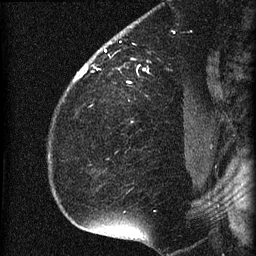
Breast MRI (dynamic contrast-enhanced), one sagittal slice; slice 48 of 60 in the series (ordered by position); dynamic contrast-enhanced series, image 2 of 4 at this slice position (ordered by acquisition); 1.5 T; TE 4.2 ms, TR 22.7 ms; 1.5 mm slice thickness; 256 × 256 image matrix, field of view 180 × 180 mm. Female patient, age 35 years. From the clinical record (not read from this slice): setting: breast cancer imaged before/during neoadjuvant chemotherapy; receptor status: HR-positive, HER2-negative.
Annotated regions visible in this slice (semi-automatic segmentation, software-assisted and operator-edited):
- analysis volume of interest (the breast-tissue region the enhancement analysis was run in; not a lesion): bounding box <69,27,199,112> (left, top, right, bottom; pixels)
- tumour enhancement mask (voxels above the 90 % enhancement threshold inside the analysis volume of interest): <74,49,145,81>